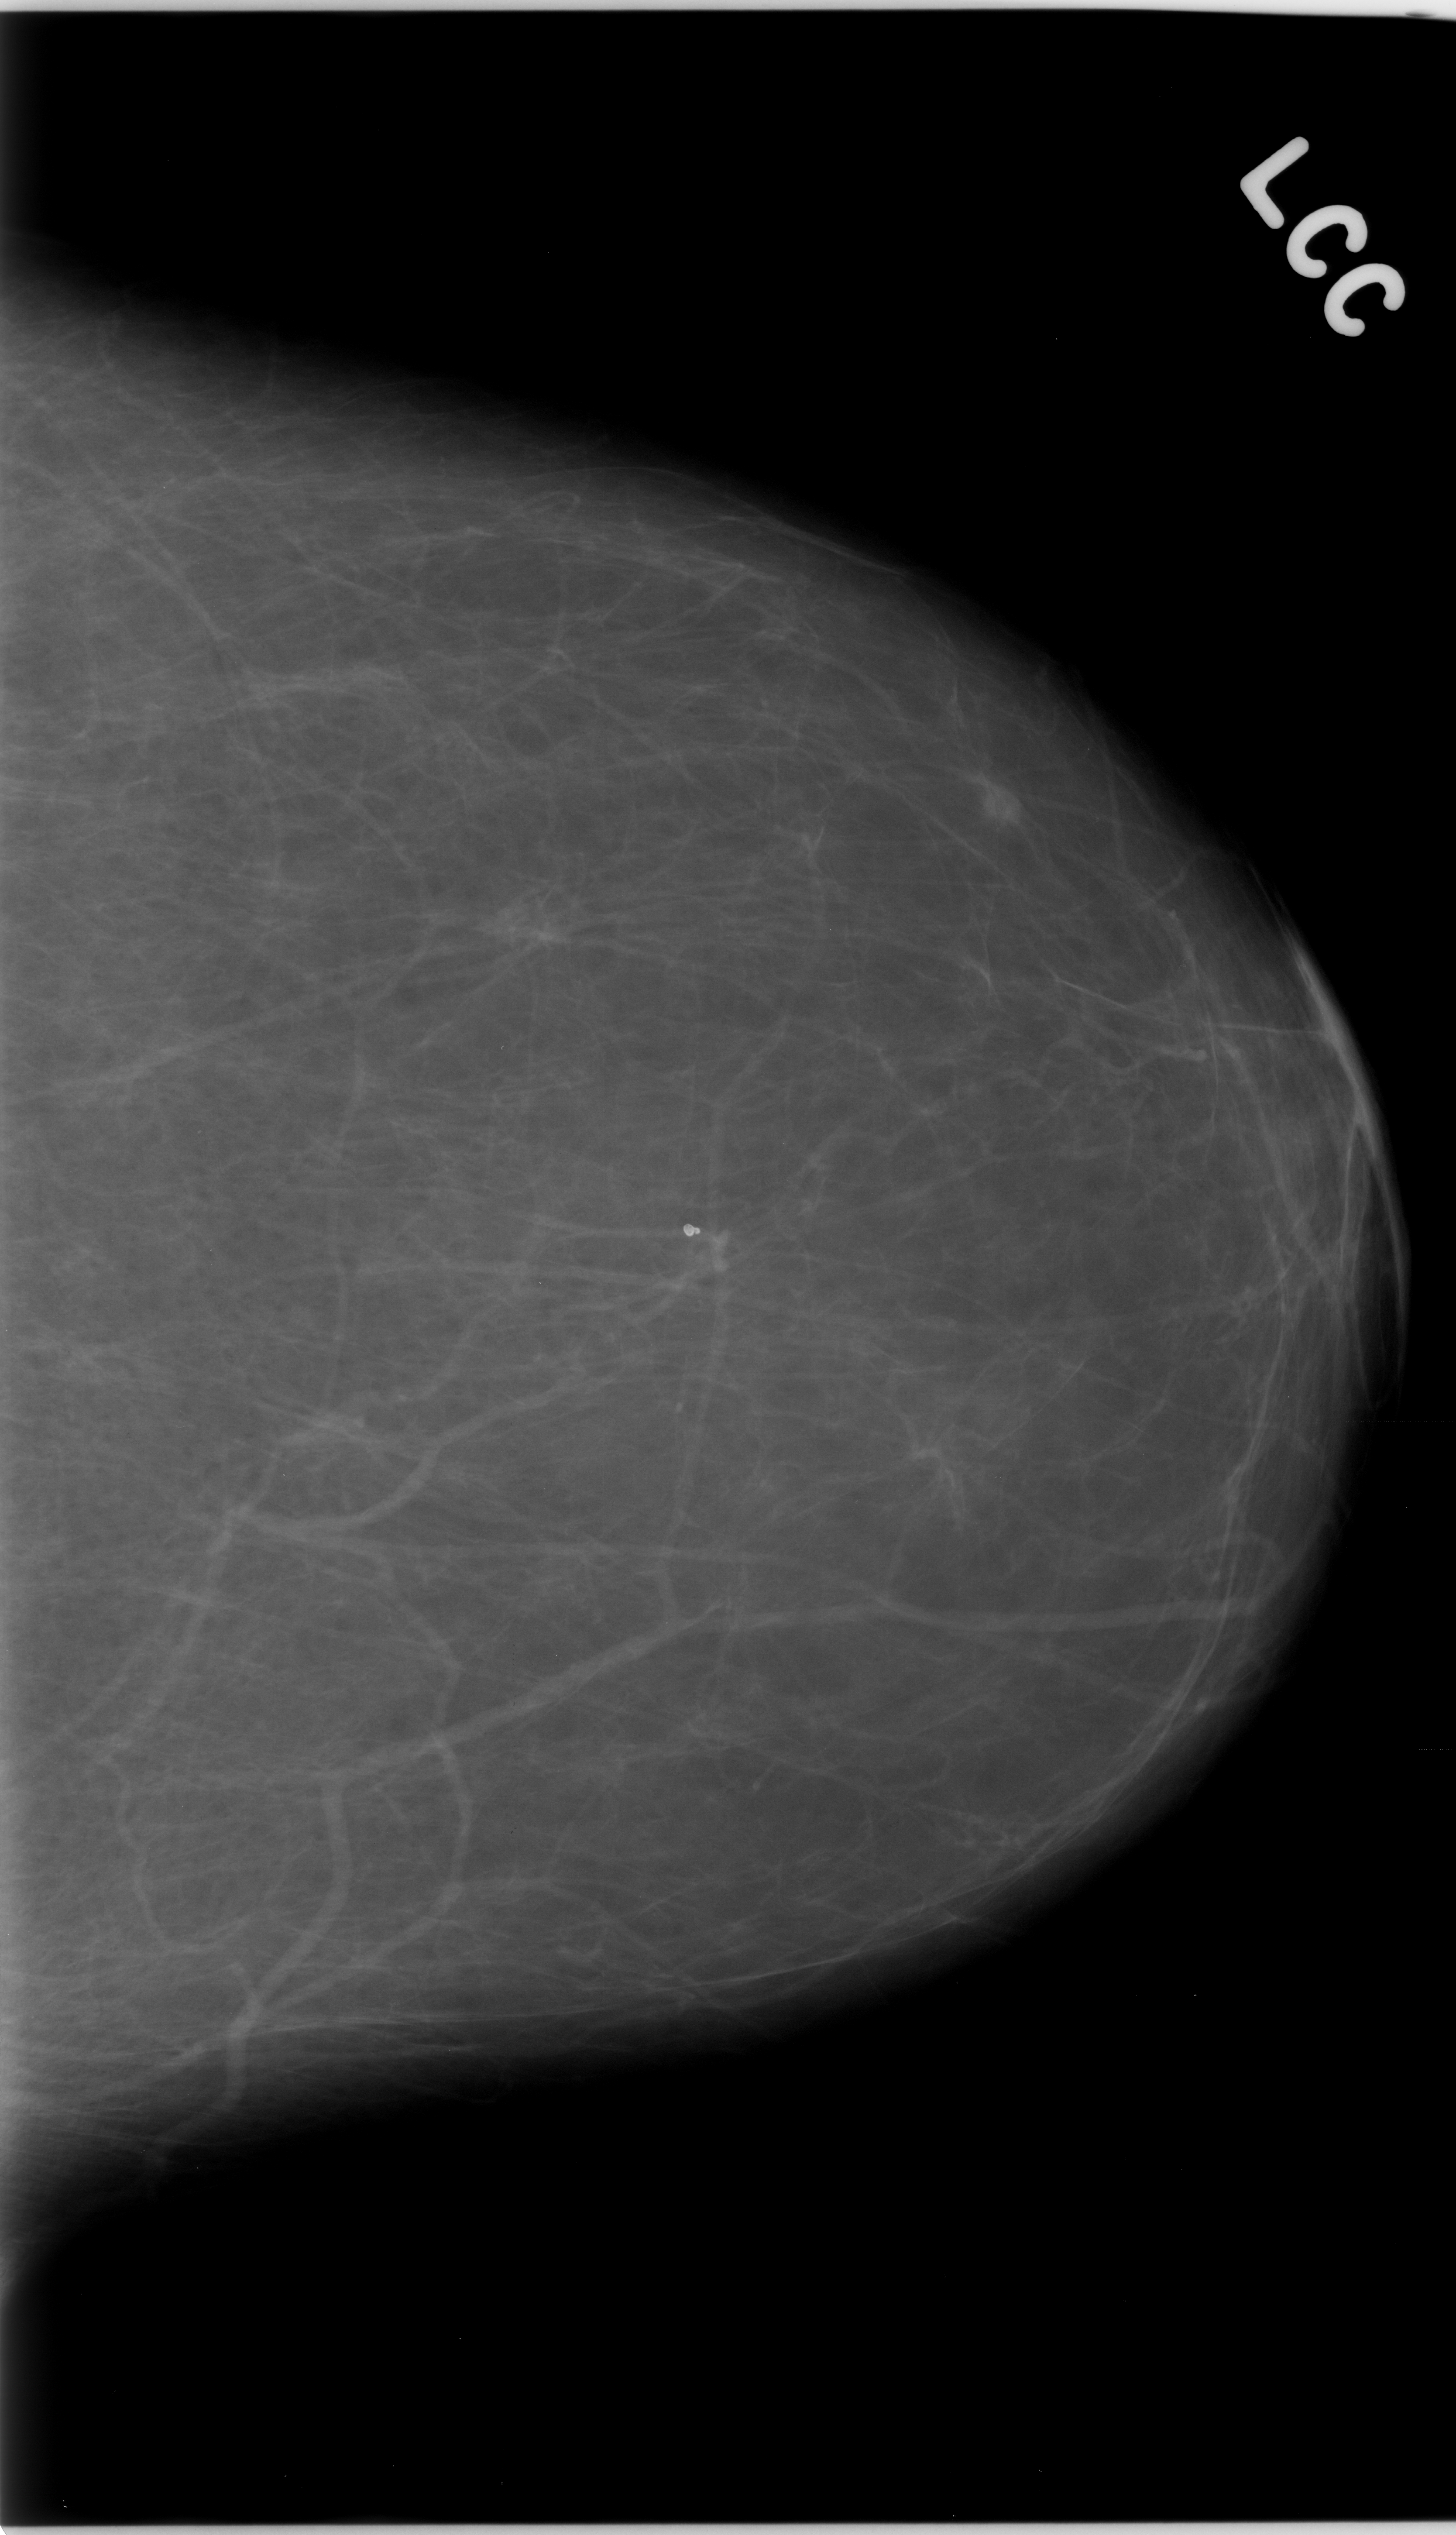
Digitized screen-film mammogram; left breast; CC view; 1456 × 2535 image matrix.
Expert-marked regions of interest on this film, with their recorded descriptors:
- mass, shape oval, margins circumscribed; BI-RADS assessment category 4; pathology (as recorded): malignant: bounding box (x1, y1, x2, y2) in pixels: (962, 760, 1046, 846)